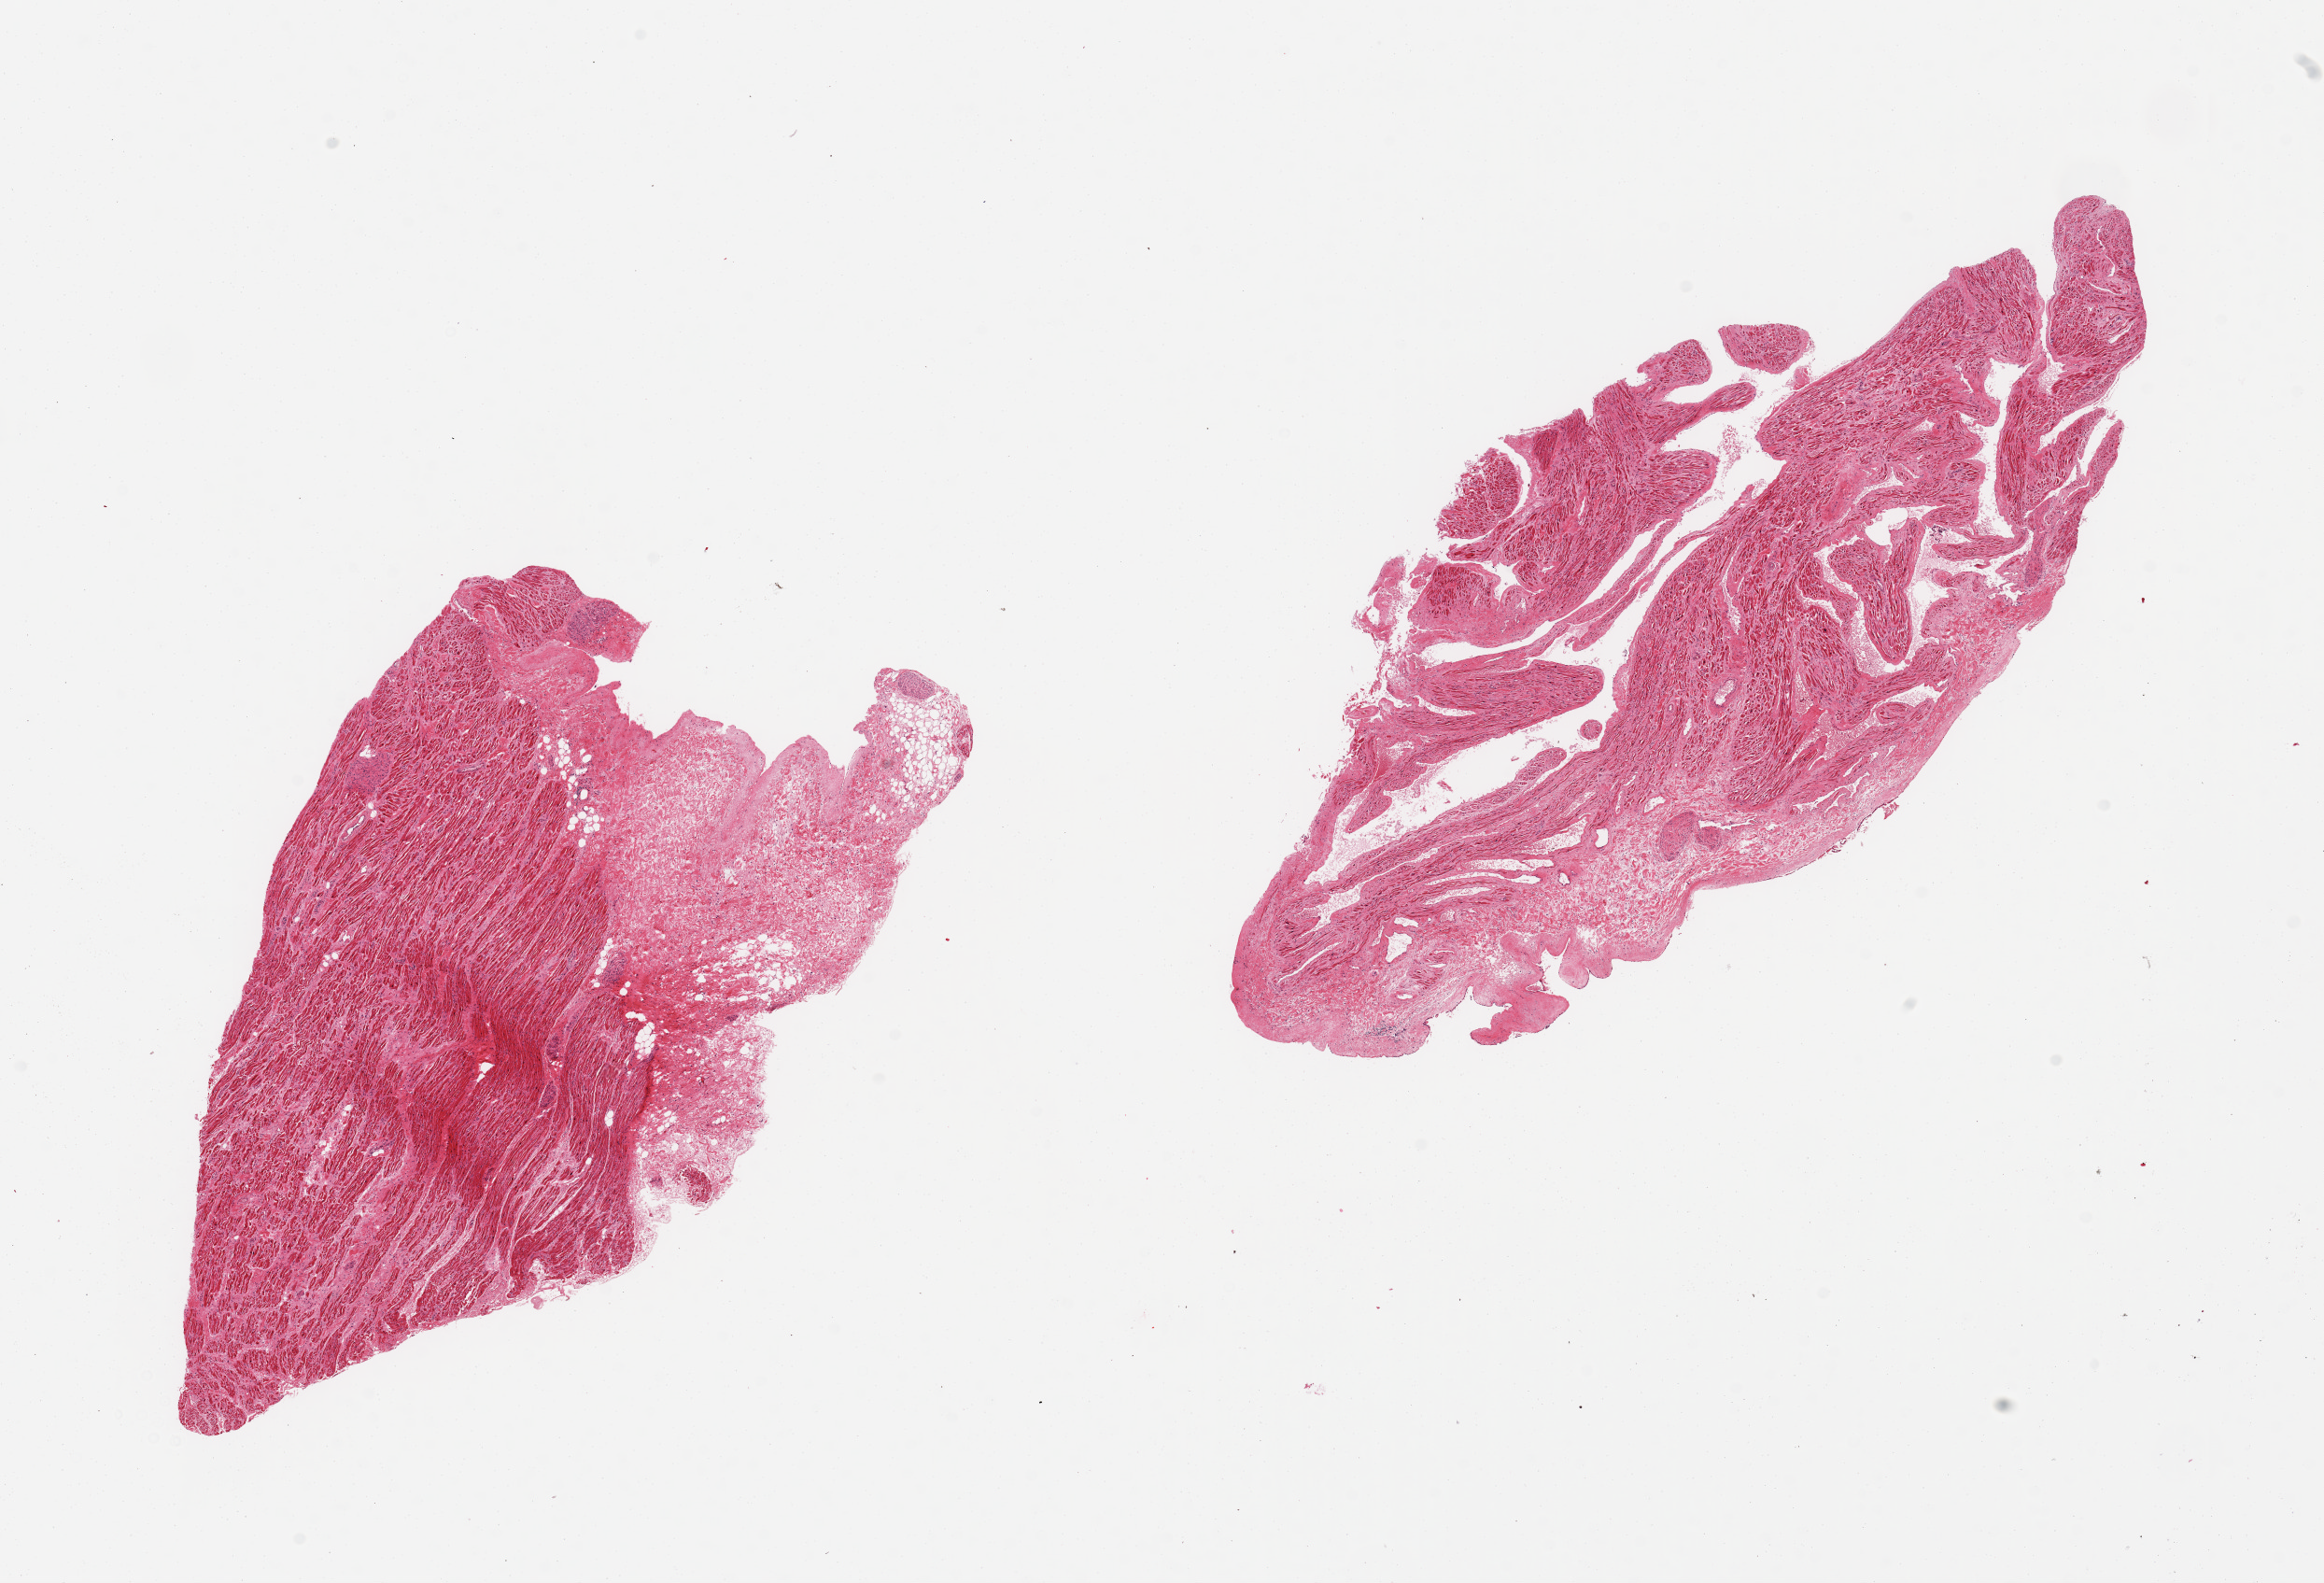
Digitized H&E-stained section — whole scanned area (about 19.7 x 13.4 mm, slide scanned at 20x) shown as a low-resolution overview. PAXgene-fixed, paraffin-embedded tissue. Target tissue: auricular appendage. Tissue donor sample. Donor: male.
* pathologist's review note for this sample: 2 pieces, no abnormalities